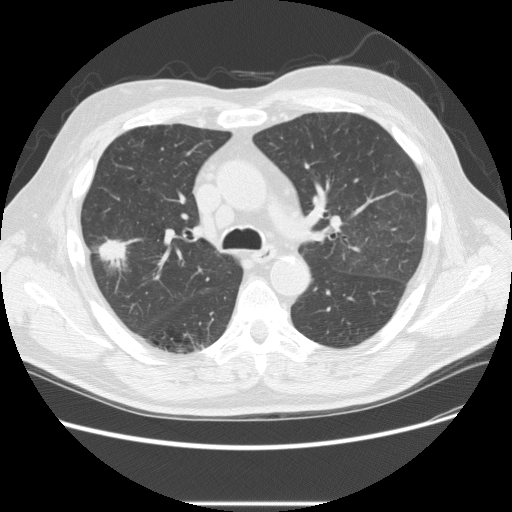
Low-dose screening chest CT, one axial slice. 120 kVp. Lung window (W 1500 / L -600 HU). 2.5 mm slice thickness. 512 × 512 image matrix, field of view 380 × 380 mm.
Outlined on this slice (outlined manually by an expert reader):
- lesion 2 (tumor, upper lobe of right lung): bounding box <97,239,128,270> (left, top, right, bottom; pixels)